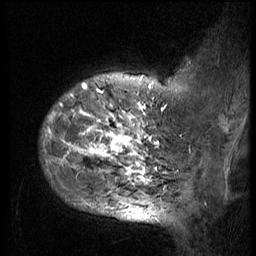
Breast MRI (dynamic contrast-enhanced), one sagittal slice. Position 11 of 56 along the scan axis. 3 images stored at this slice position (order not interpretable as contrast timing). 1.5 T. TE 4.2 ms, TR 9 ms. 2.5 mm slice thickness. 256 × 256 image matrix. Female patient, age 49 years. Case-level facts recorded for this patient, not image findings: setting: breast cancer imaged before/during neoadjuvant chemotherapy; receptor status: HER2-positive.
Annotated regions visible in this slice (semi-automatically segmented with operator editing):
- analysis volume of interest (the breast-tissue region the enhancement analysis was run in; not a lesion): bounding box (x1, y1, x2, y2) in pixels: (38, 85, 165, 207)
- tumour enhancement mask (voxels above the 140 % enhancement threshold inside the analysis volume of interest): (43, 85, 157, 207)